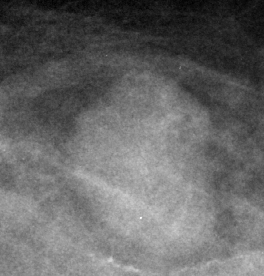
Crop from a digitized film mammogram around one marked abnormality, right breast, CC view.
- Mass, shape oval, margins circumscribed; BI-RADS assessment category 3; subtlety rating 5 on a 1 (subtle) to 5 (obvious) scale; pathology (as recorded): benign.